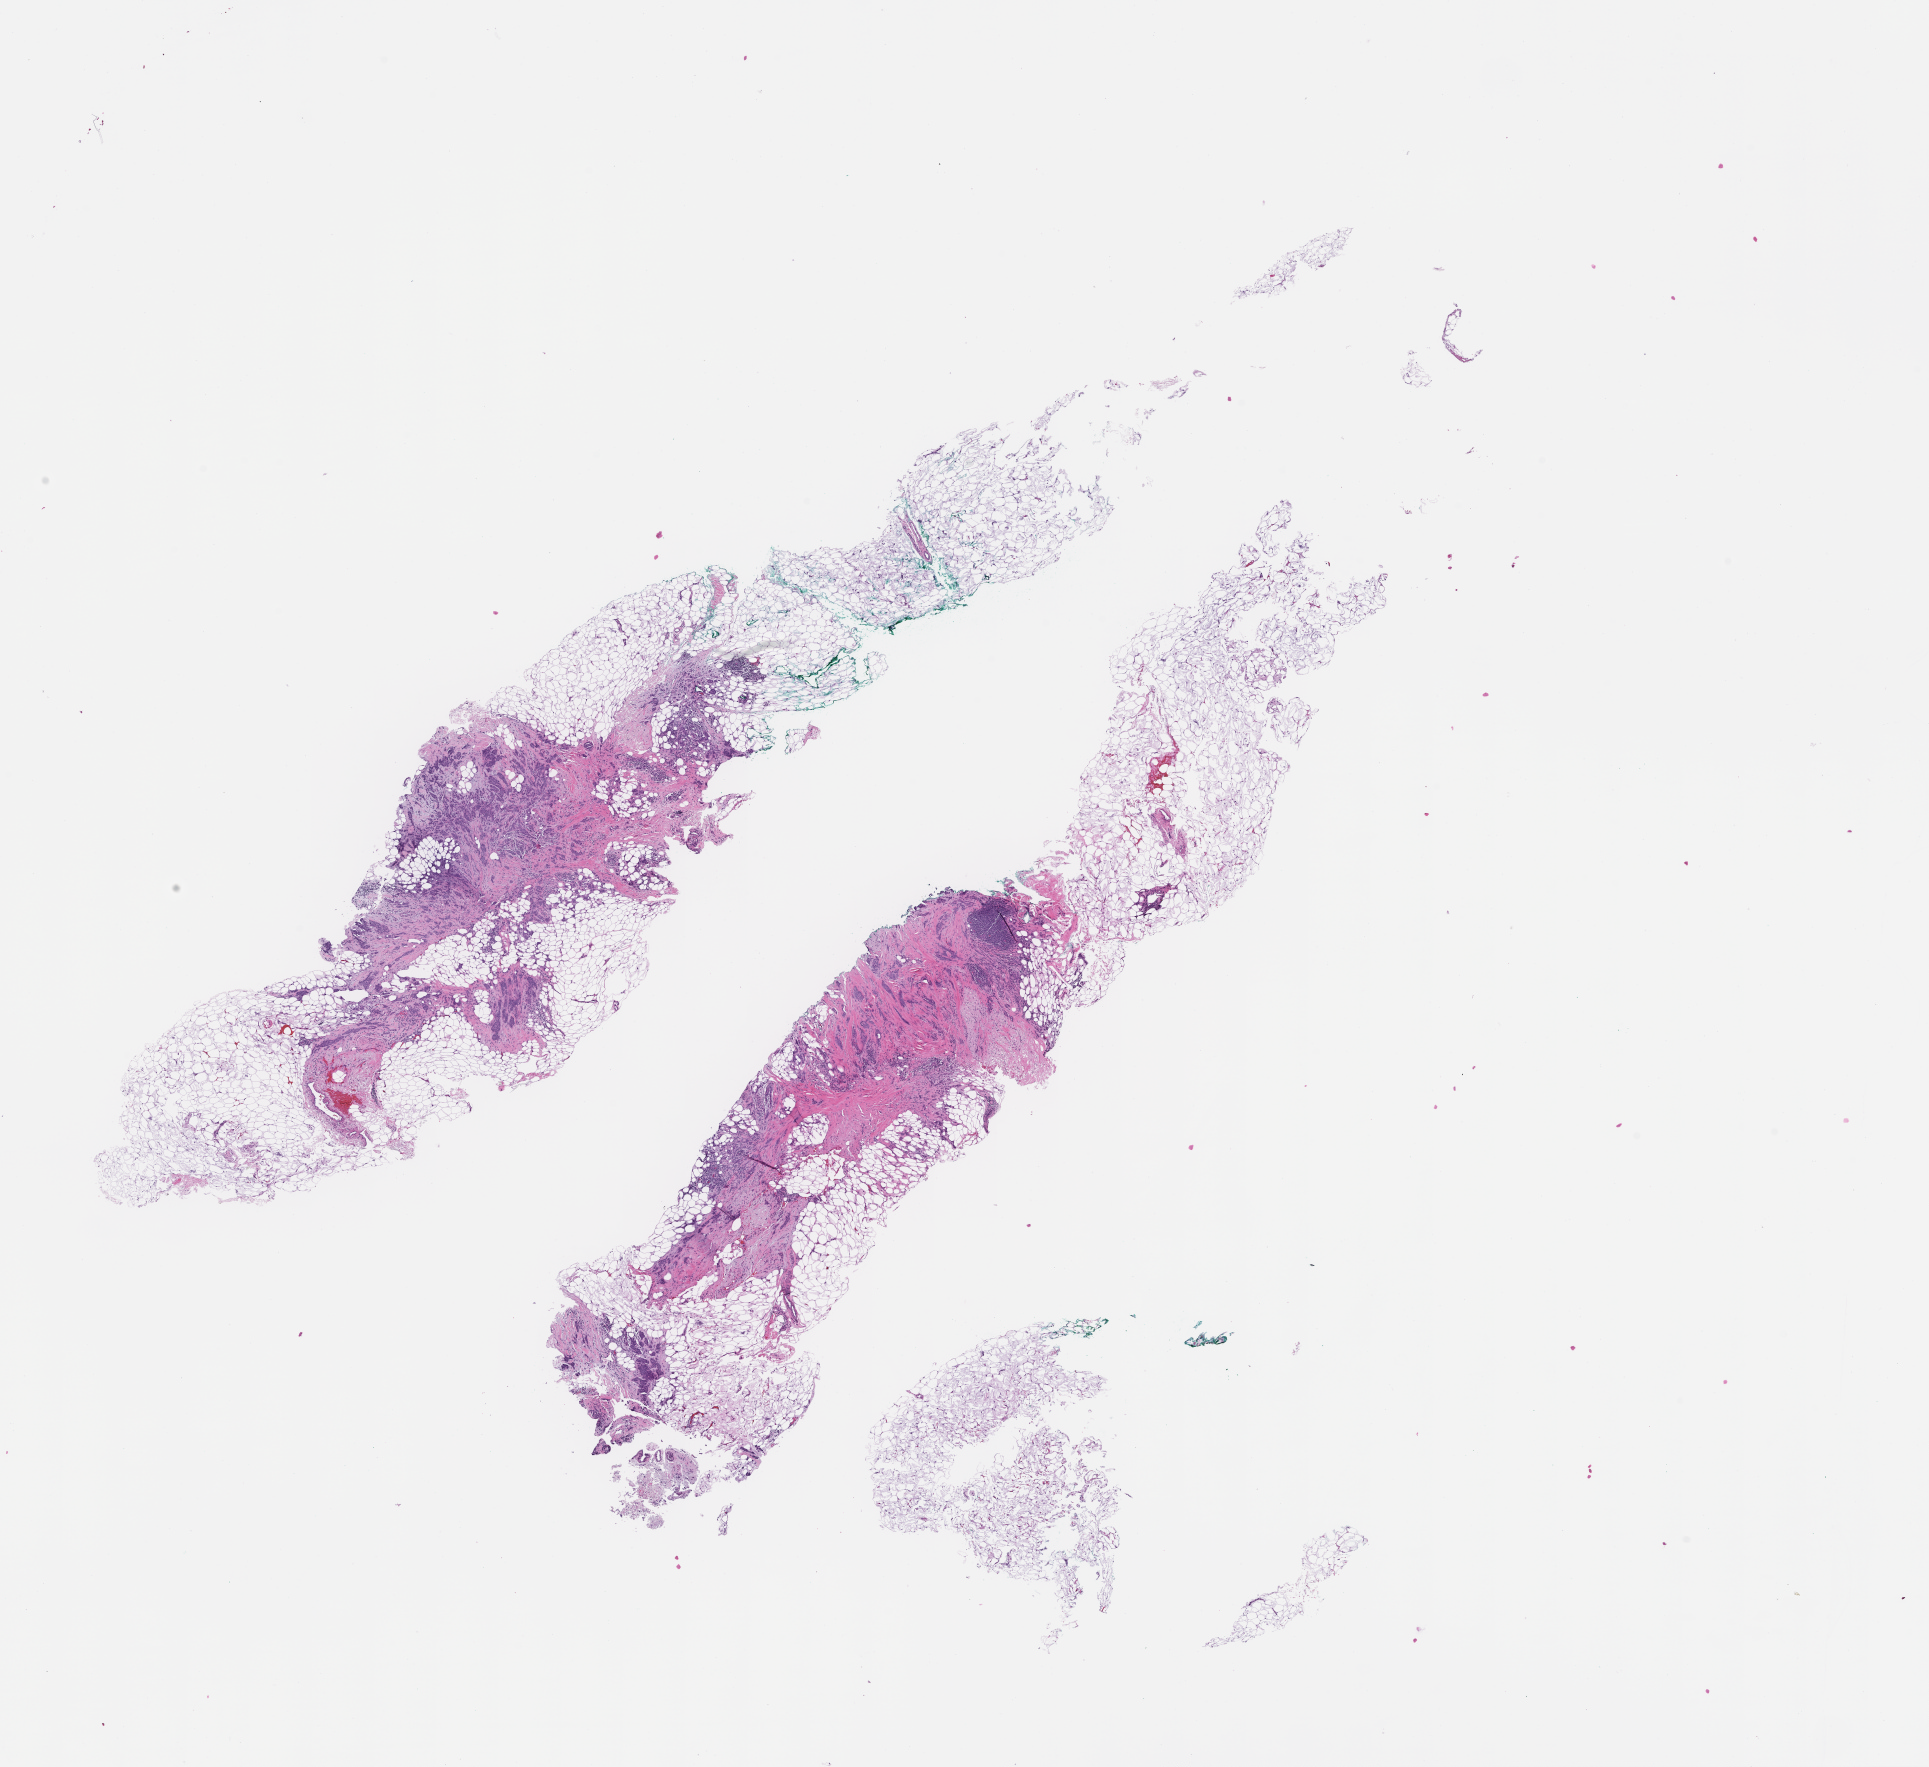
Digitized H&E-stained section — shown as a low-resolution overview of the whole scanned area (about 15.6 x 14.3 mm), formalin-fixed, paraffin-embedded (FFPE) tissue, tissue site: breast, specimen time point: archival tissue. Female patient.
• from a patient with: Invasive Breast Carcinoma